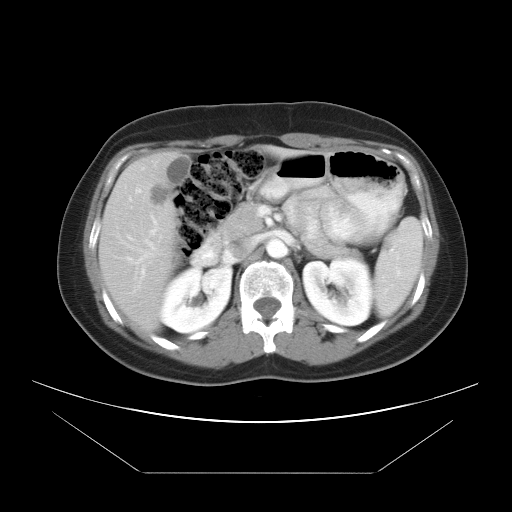
Contrast-enhanced abdominal CT, one axial slice; position 21 of 34 along the scan axis; 120 kVp; intravenous contrast given; soft-tissue window (W 400 / L 40 HU); 7.5 mm slice thickness; 512 × 512 image matrix, field of view 410 × 410 mm. Female patient, age 38 years. Case-level facts recorded for this patient, not image findings: diagnosis: colorectal cancer liver metastases, imaged before liver resection; multiple liver metastases: yes; largest metastasis: 3.1 cm.
Outlined on this slice (manually delineated by an expert):
- liver: bounding box (x1, y1, x2, y2) in pixels: (99, 153, 178, 332)
- portal vein (with intrahepatic branches): (117, 206, 216, 284)
- liver metastasis: (146, 181, 174, 207)